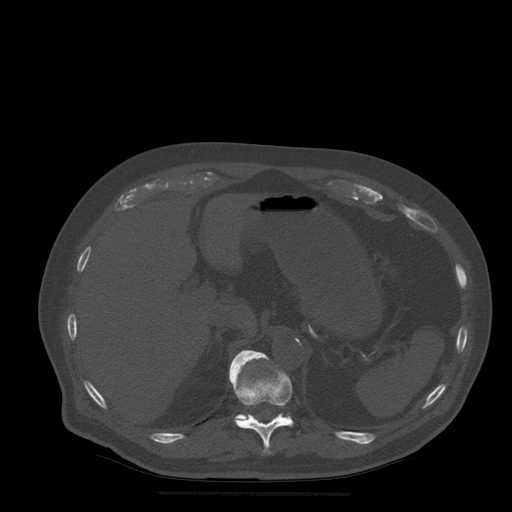
CT including the spine, one axial slice. Slice 239 of 522 in the series (ordered by position). Bone window (W 1800 / L 400 HU). 1.25 mm slice thickness. 512 × 512 image matrix. Patient age 72 years. Case-level facts recorded for this patient, not image findings: primary cancer: prostate.
Outlined on this slice (semi-automatic segmentation, software-assisted and operator-edited):
- T11 vertebra: bounding box (x1, y1, x2, y2) in pixels: (231, 352, 294, 454)
- T12 vertebra: (229, 350, 270, 420)